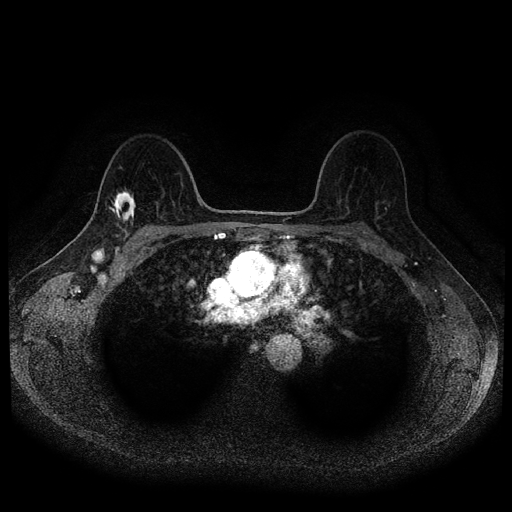
Breast MRI (dynamic contrast-enhanced, multi-phase), one axial slice. Position 70 of 116 along the scan axis. Dynamic contrast-enhanced series, time point 2 of 5 at this slice position (early post-contrast). 1.5 T. TE 2.6 ms, TR 5.4 ms. 2 mm slice thickness. 512 × 512 image matrix, field of view 340 × 340 mm. Patient: female, 49 years.
Outlined on this slice (semi-automatic segmentation, software-assisted and operator-edited):
- breast lesion (labelled 'tumour' in the annotation; benign lesions carry a separate 'benign' label): bounding box [x1, y1, x2, y2] px = [111, 189, 136, 227]